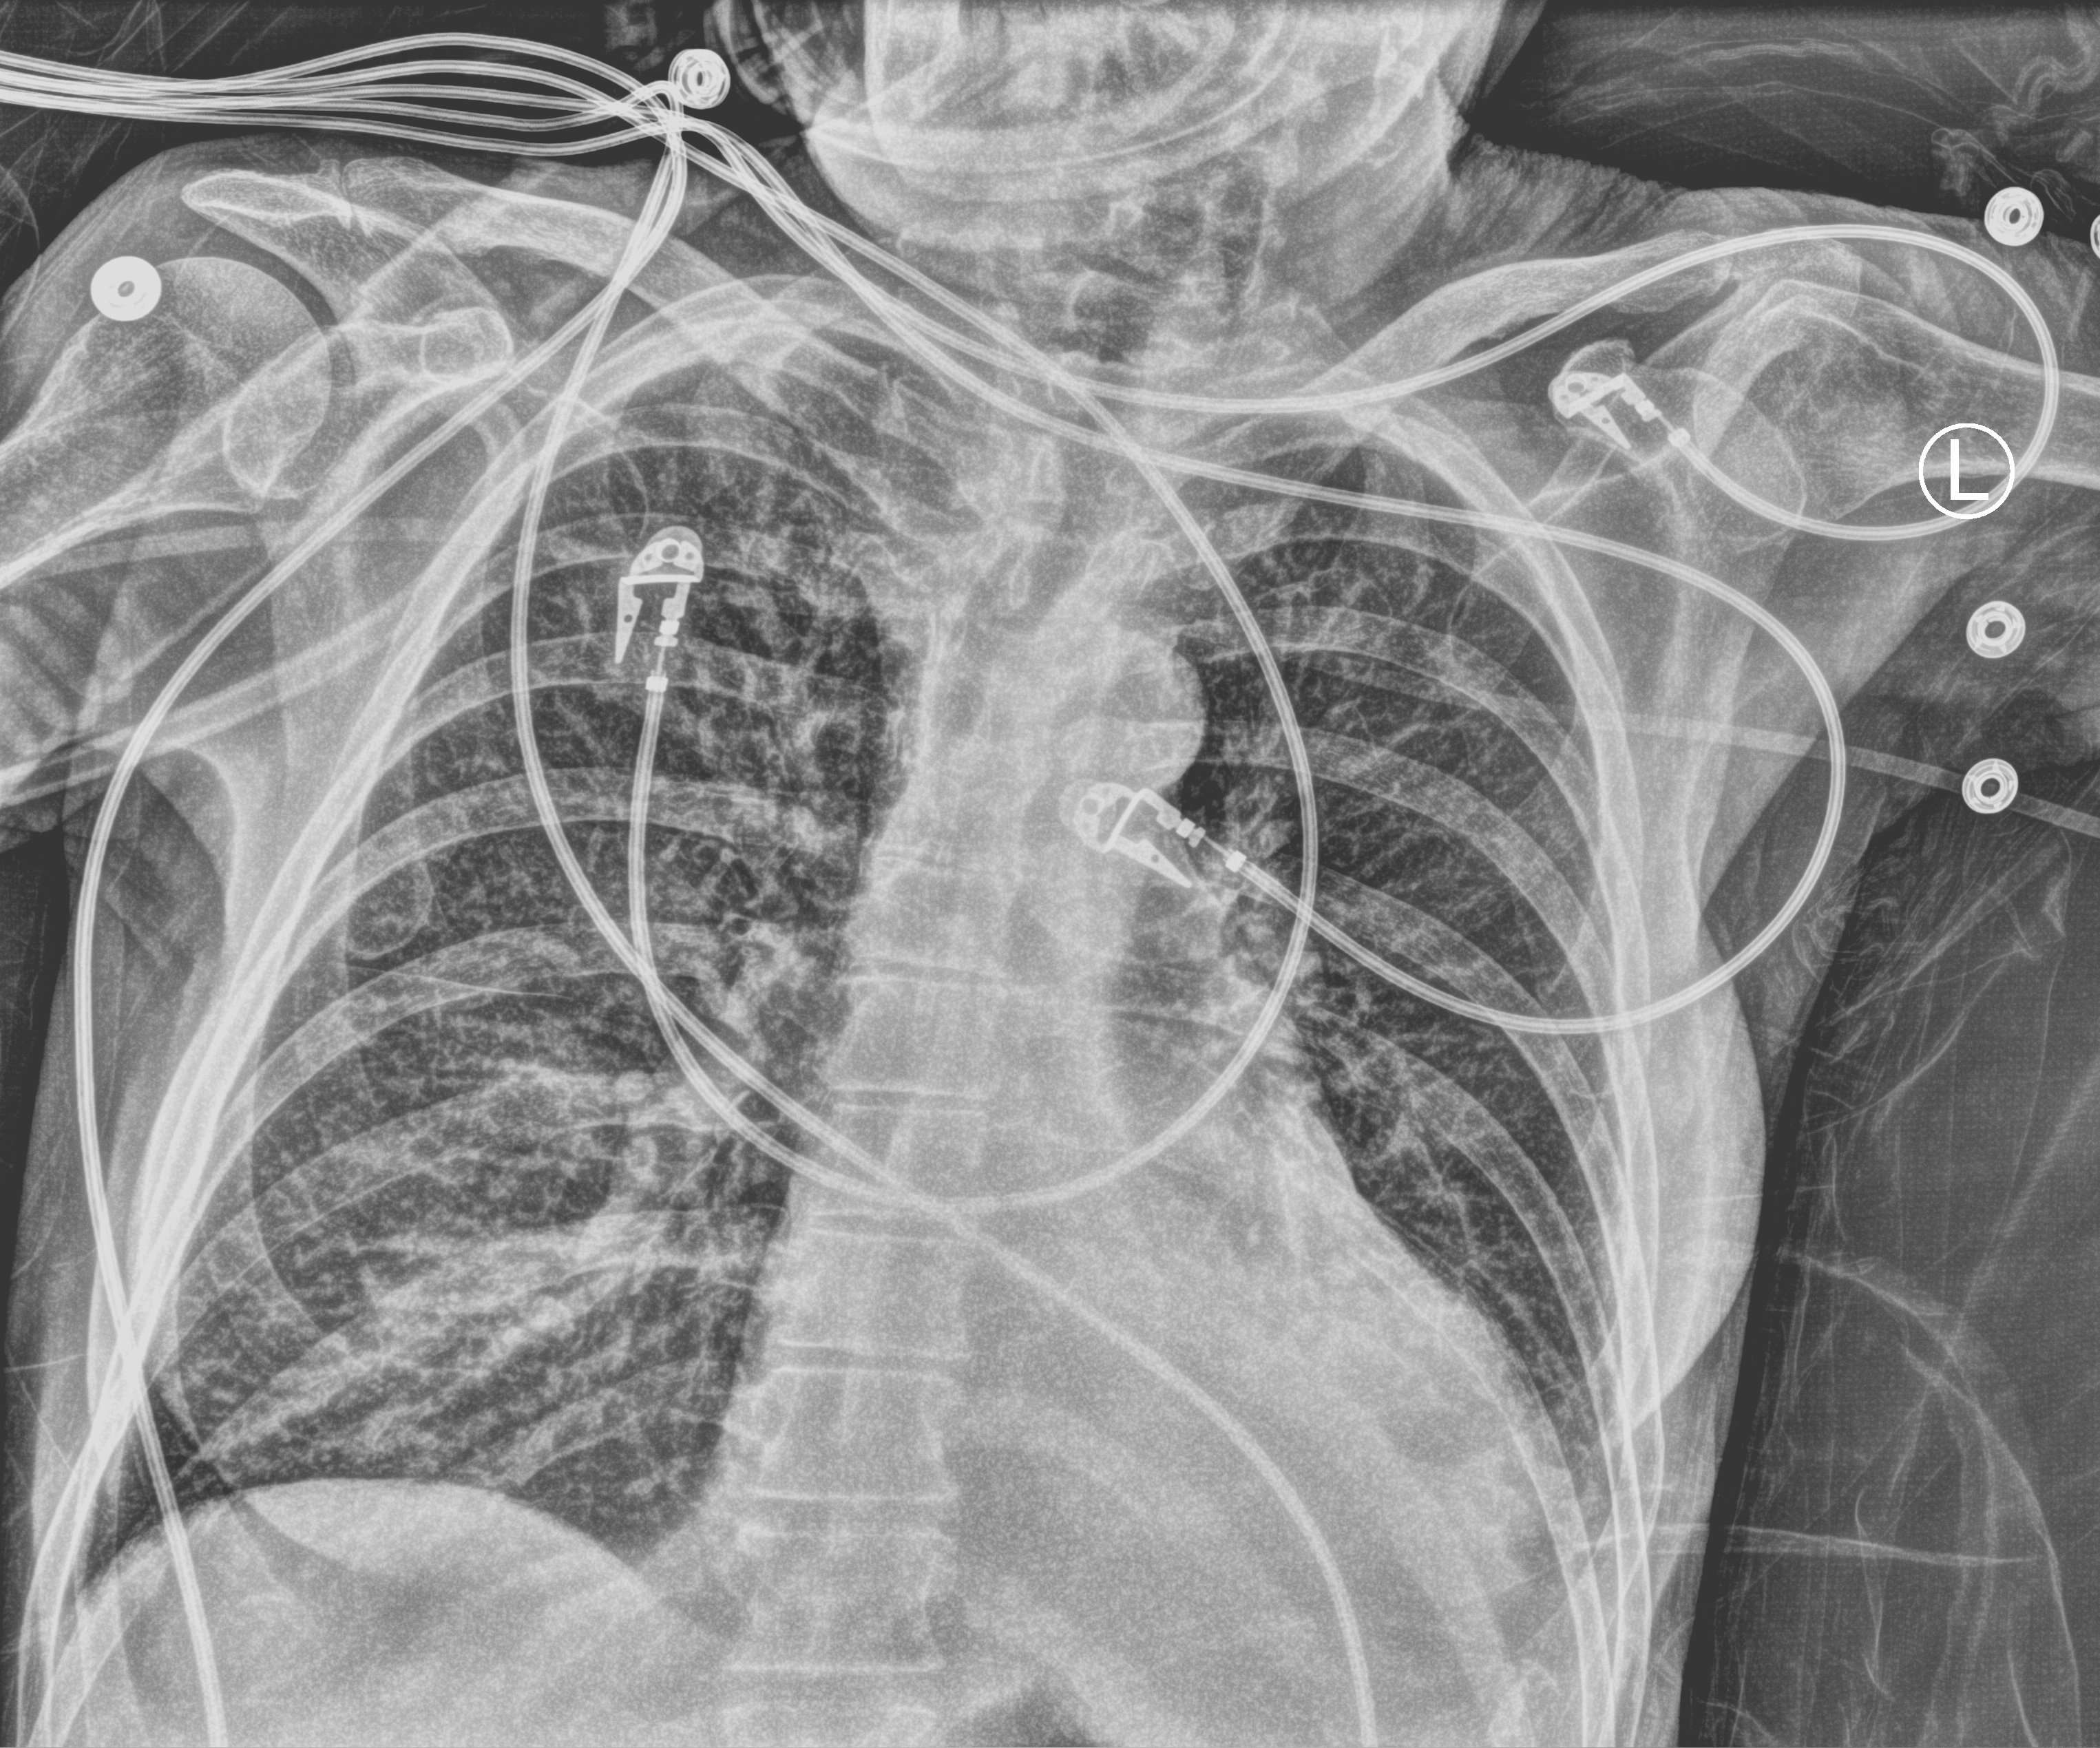
Portable chest radiograph; anteroposterior (AP) projection. Patient hospitalised with COVID-19; female, aged 60–74 years.
Admission-level facts for this patient (not findings on this image; timing relative to this image not recorded): admitted to intensive care during this hospital stay: yes; mechanically ventilated during this hospital stay: yes.